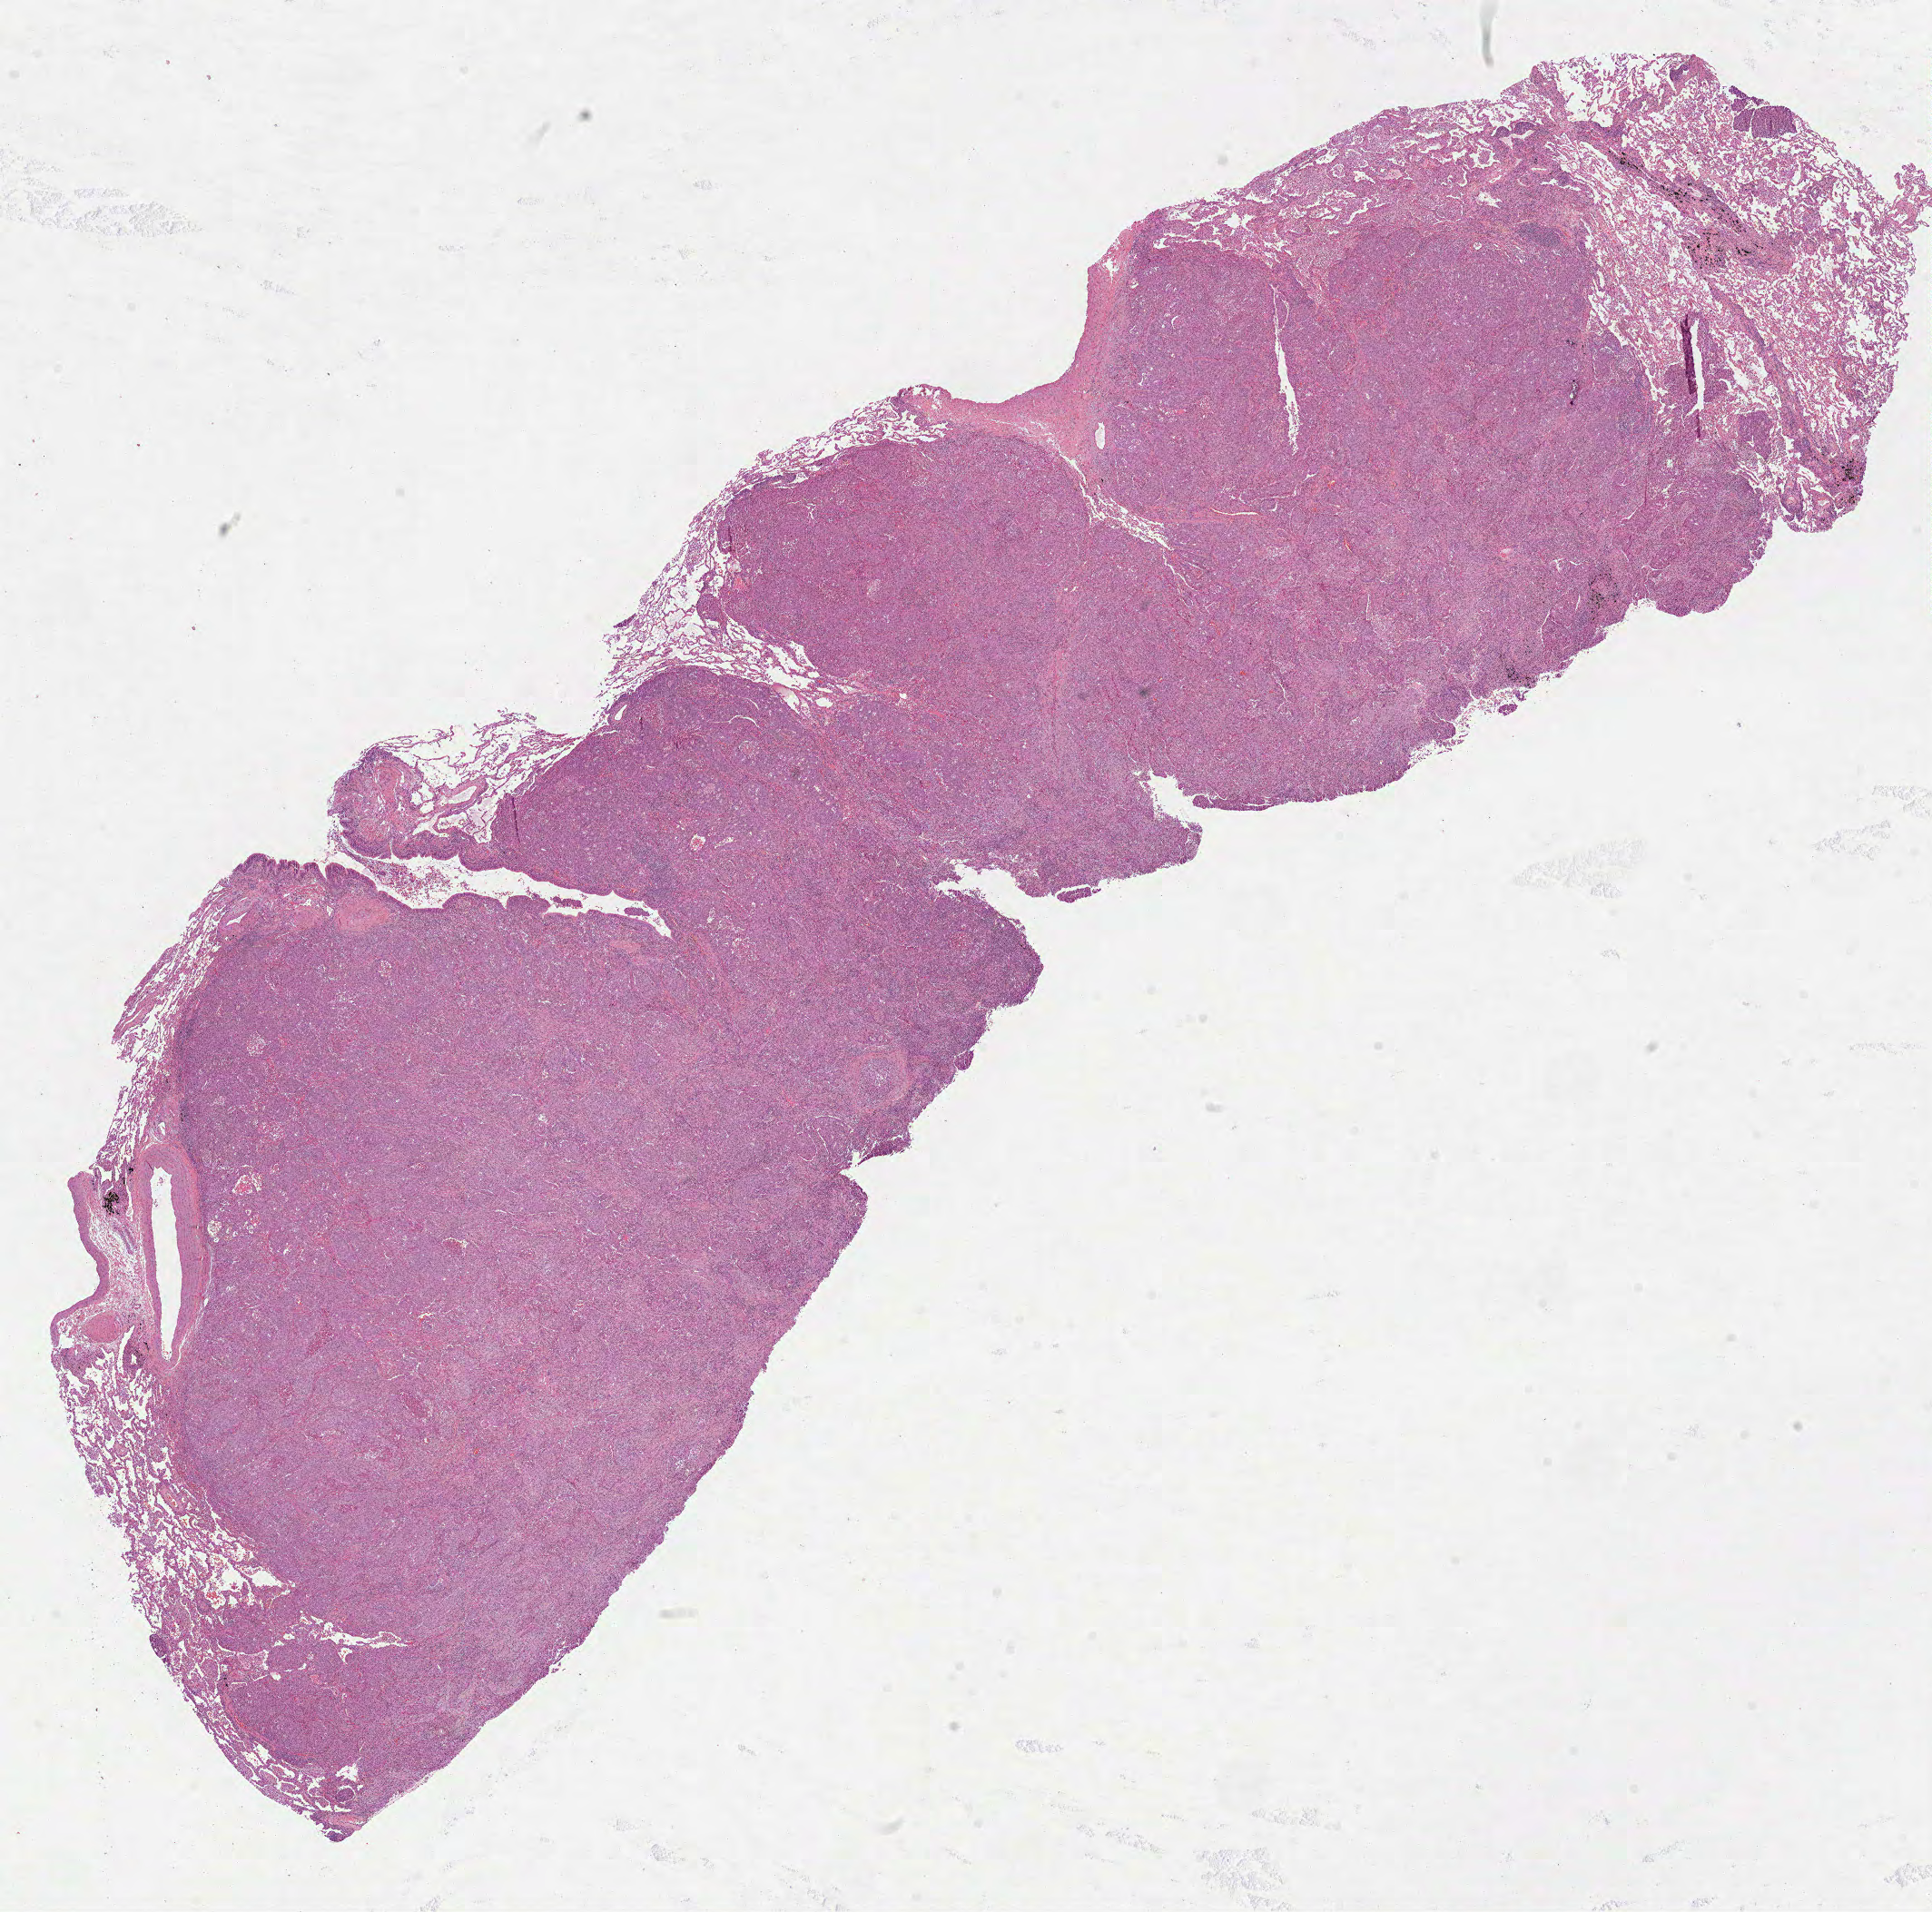
Digitized H&E-stained tissue section (whole slide) — low-resolution overview of the scanned area, about 17.2 x 17.0 mm. FFPE section. Sample: primary tumour, lung. Female, age 59 years at initial diagnosis.
• AJCC pathologic stage: IIB (6th edition)
• pathologic diagnosis: Adenocarcinoma, NOS (upper lobe, lung)
• laterality: left
• TNM: T2 N1 M0